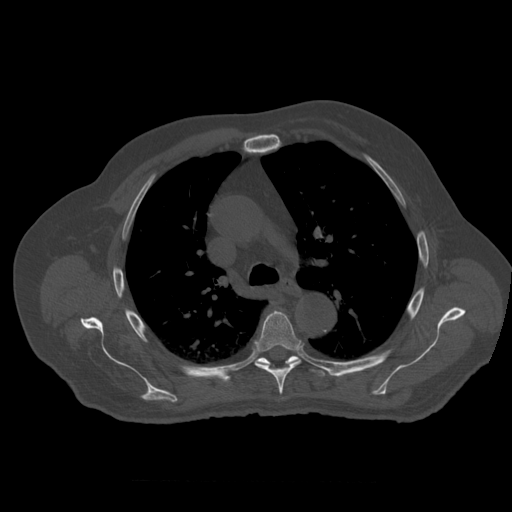
CT including the spine, one axial slice. Position 395 of 399 along the scan axis. Reconstruction kernel STANDARD. Bone window (W 1800 / L 400 HU). 1.25 mm slice thickness. 512 × 512 image matrix. Patient age 73 years. From the clinical record (not read from this slice): primary cancer: prostate; vertebrae with lytic lesions (as recorded): L2.
Outlined on this slice (semi-automatic segmentation, software-assisted and operator-edited):
- T5 vertebra: box from (x=254, y=312) to (x=302, y=400) px
- T6 vertebra: (x=244, y=356)–(x=326, y=377)